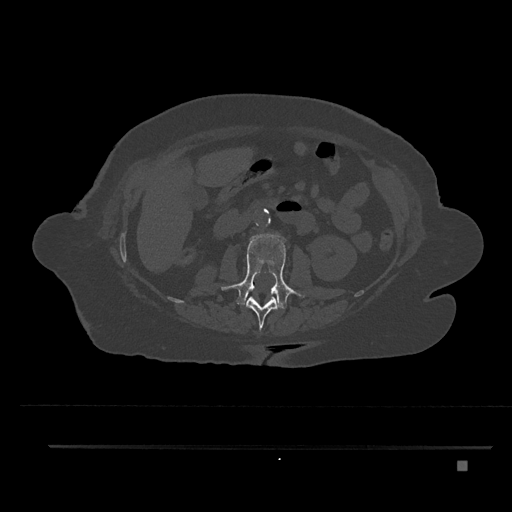
CT including the spine, one axial slice; position 187 of 797 along the scan axis; 120 kVp; bone window (W 1800 / L 400 HU); 512 × 512 image matrix, field of view 437 × 437 mm. Female patient, age 76 years. Case-level facts recorded for this patient, not image findings: primary cancer: lung; vertebrae with lytic lesions (as recorded): T11, L3.
Structures marked on this image (semi-automatically segmented with operator editing):
- L1 vertebra: bounding box <246,295,279,330> (left, top, right, bottom; pixels)
- L2 vertebra: <221,234,304,310>